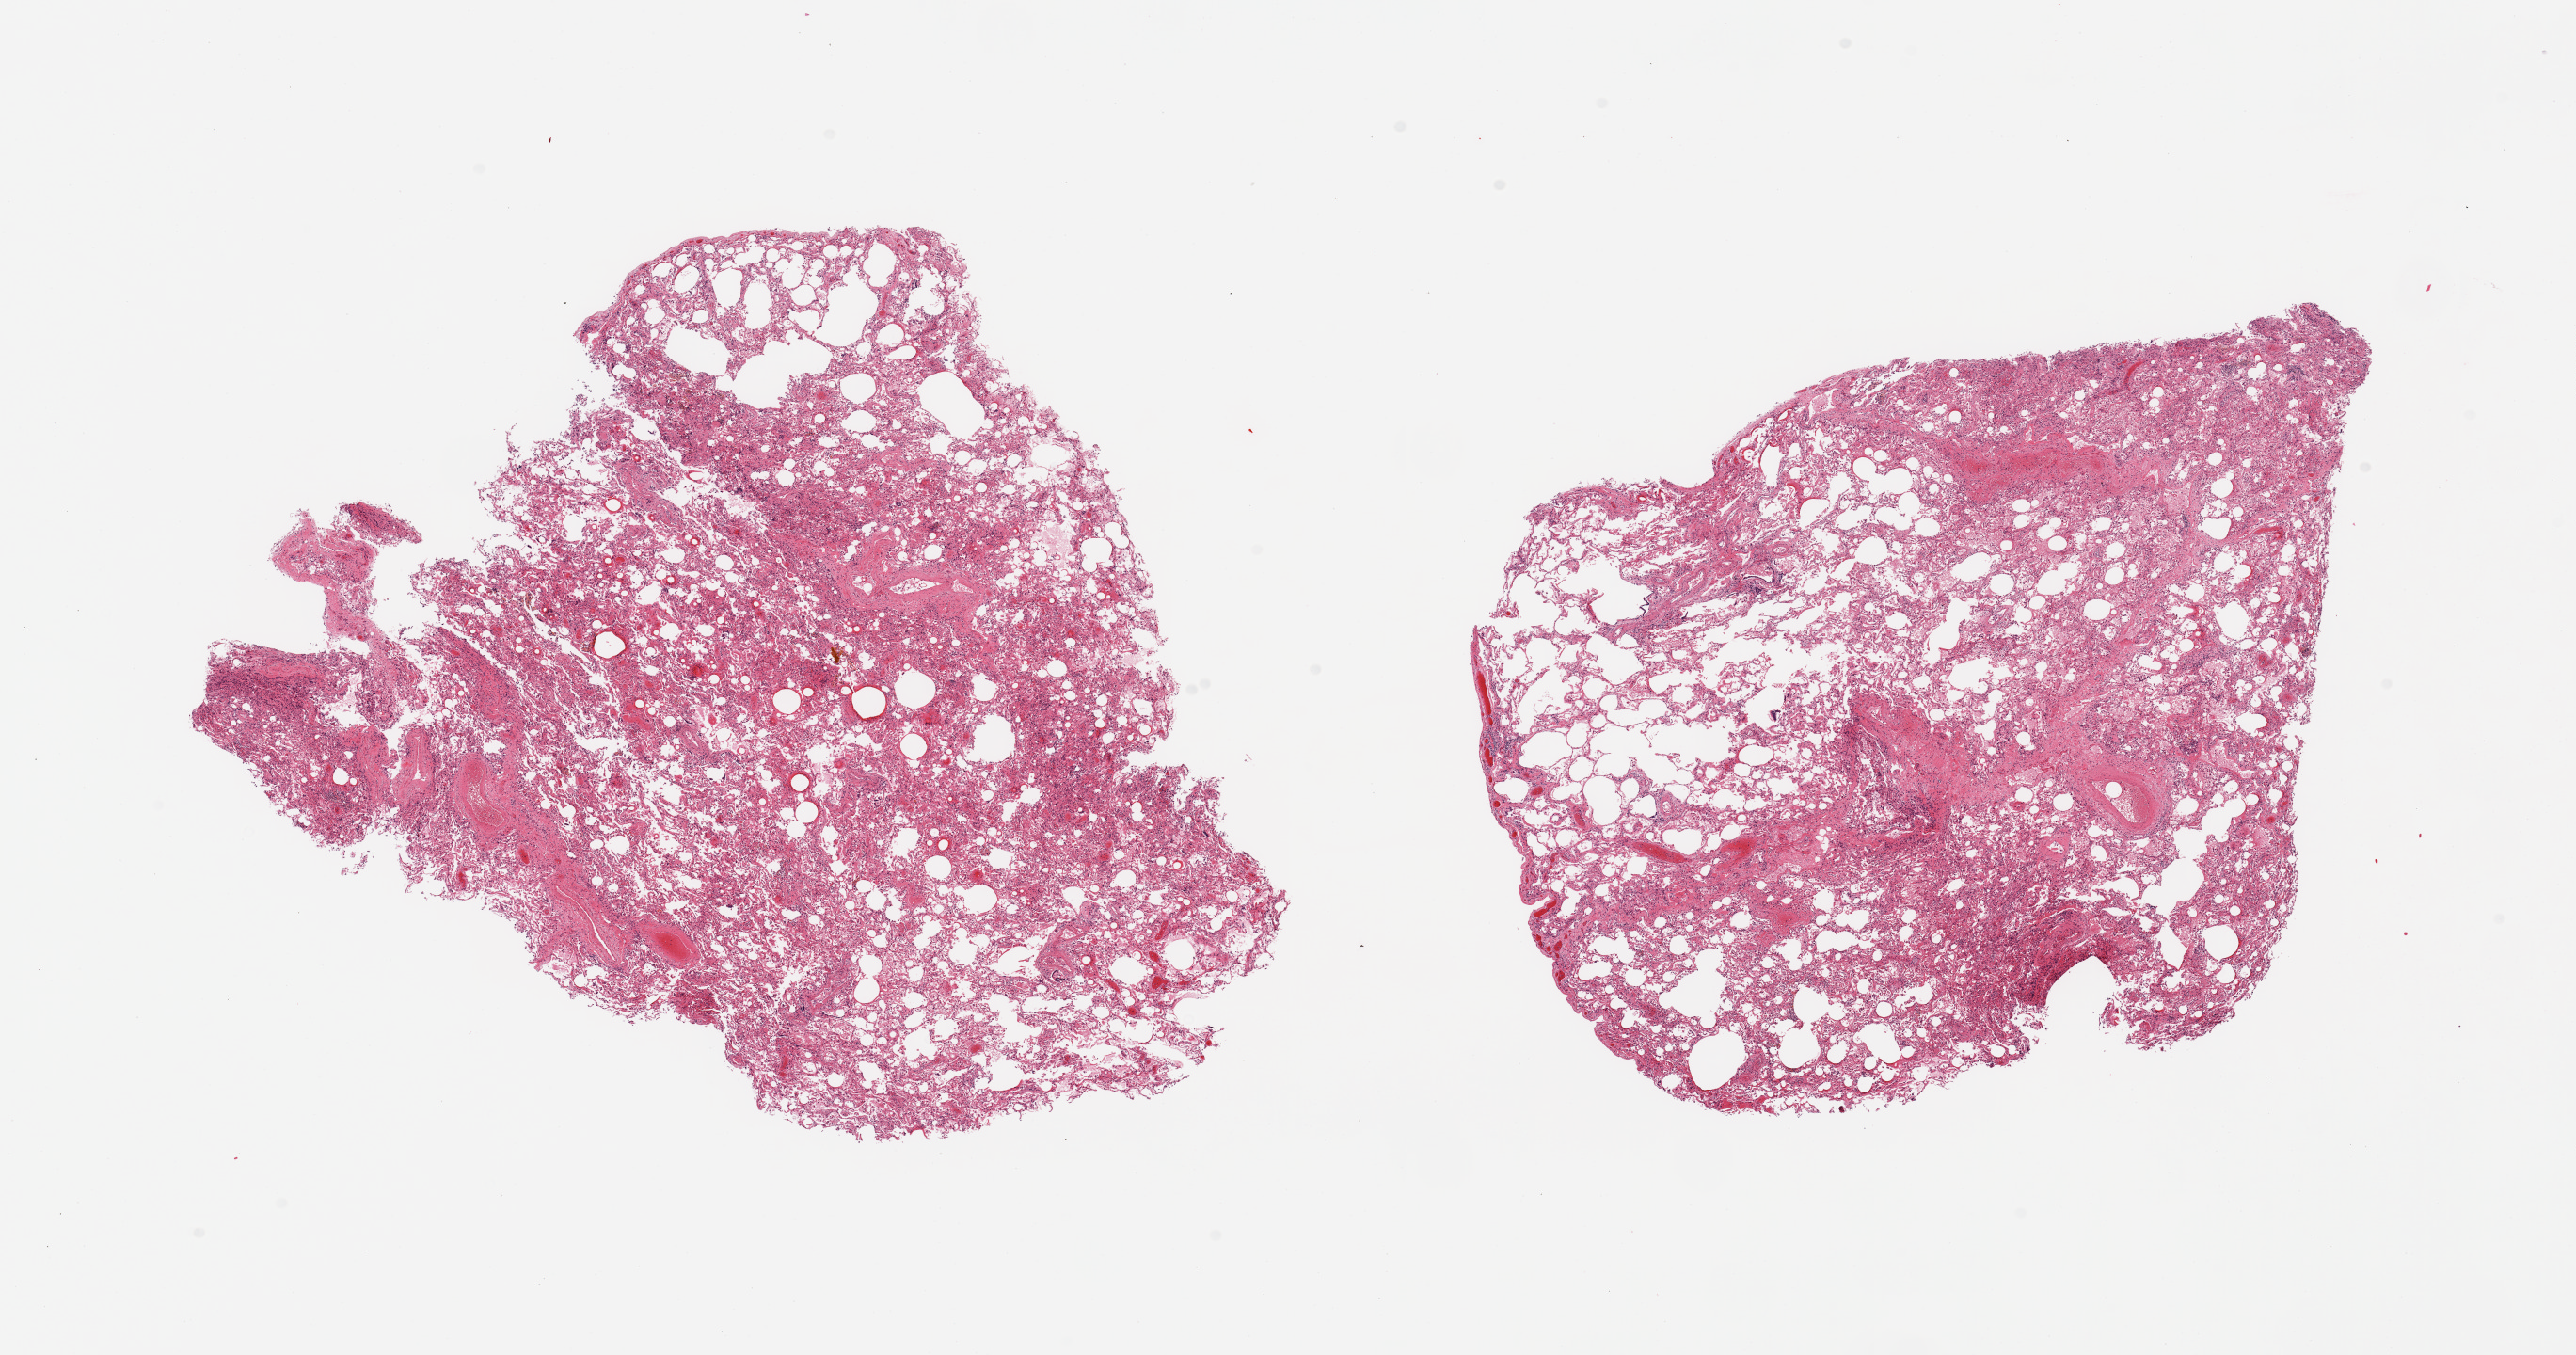
Whole-slide image, H&E stain, a low-resolution overview of the entire scanned area, about 21.7 x 11.4 mm (from a 20x scan); PAXgene-fixed, paraffin-embedded tissue; section of lung (target tissue); donor tissue sample. Female donor.
* pathologist's review note for this sample: 2 pieces; patchy pneumonia affects 30%